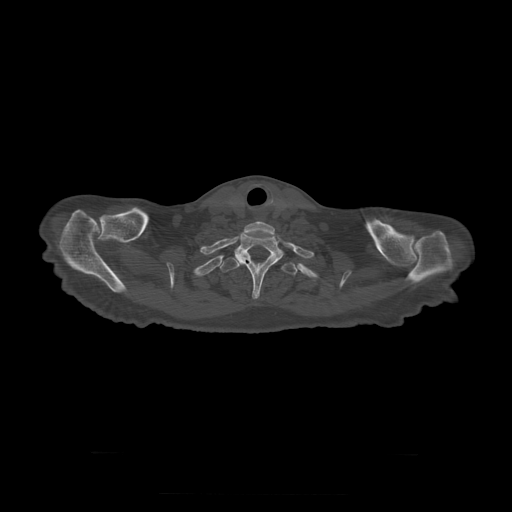
CT including the spine, one axial slice; slice 285 of 397 in the series (ordered by position); 120 kVp; bone window (W 1800 / L 400 HU); 512 × 512 image matrix. Patient age 73 years. Case-level facts recorded for this patient, not image findings: primary cancer: prostate.
Structures marked on this image (semi-automatic segmentation, software-assisted and operator-edited):
- T1 vertebra: bounding box [x1, y1, x2, y2] px = [235, 231, 283, 298]
- T2 vertebra: [221, 257, 298, 276]